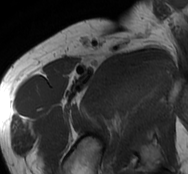
MRI of an extremity soft-tissue mass, one axial slice. Position 70 of 93 along the scan axis. MR volume resampled by the dataset authors to the PET/CT grid (not the native acquisition matrix). 188 × 174 image matrix, field of view 184 × 170 mm. Male patient. From the clinical record (not read from this slice): histological type: undifferentiated - pleiomorphic; grade: high; site of the primary tumour: right thigh.
Structures marked on this image (expert contour drawn on MRI and transferred to this co-registered scan by the dataset authors):
- gross tumour volume including surrounding oedema: bounding box <109,51,176,123> (left, top, right, bottom; pixels)
- gross tumour volume (mass): <109,56,172,116>